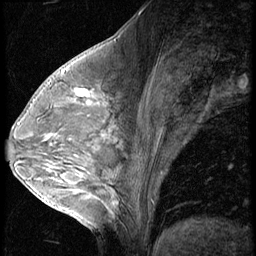
Breast MRI (dynamic contrast-enhanced), one sagittal slice. Slice 29 of 56 in the series (ordered by position). 3 images stored at this slice position (order not interpretable as contrast timing). 1.5 T. TE 4.2 ms, TR 9 ms. 256 × 256 image matrix. Patient: female, 54 years. Case-level facts recorded for this patient, not image findings: setting: breast cancer imaged before/during neoadjuvant chemotherapy; receptor status: triple-negative.
Outlined on this slice (semi-automatically segmented with operator editing):
- analysis volume of interest (the breast-tissue region the enhancement analysis was run in; not a lesion): box from (x=62, y=80) to (x=115, y=128) px
- tumour enhancement mask (voxels above the 140 % enhancement threshold inside the analysis volume of interest): (x=76, y=89)–(x=89, y=97)